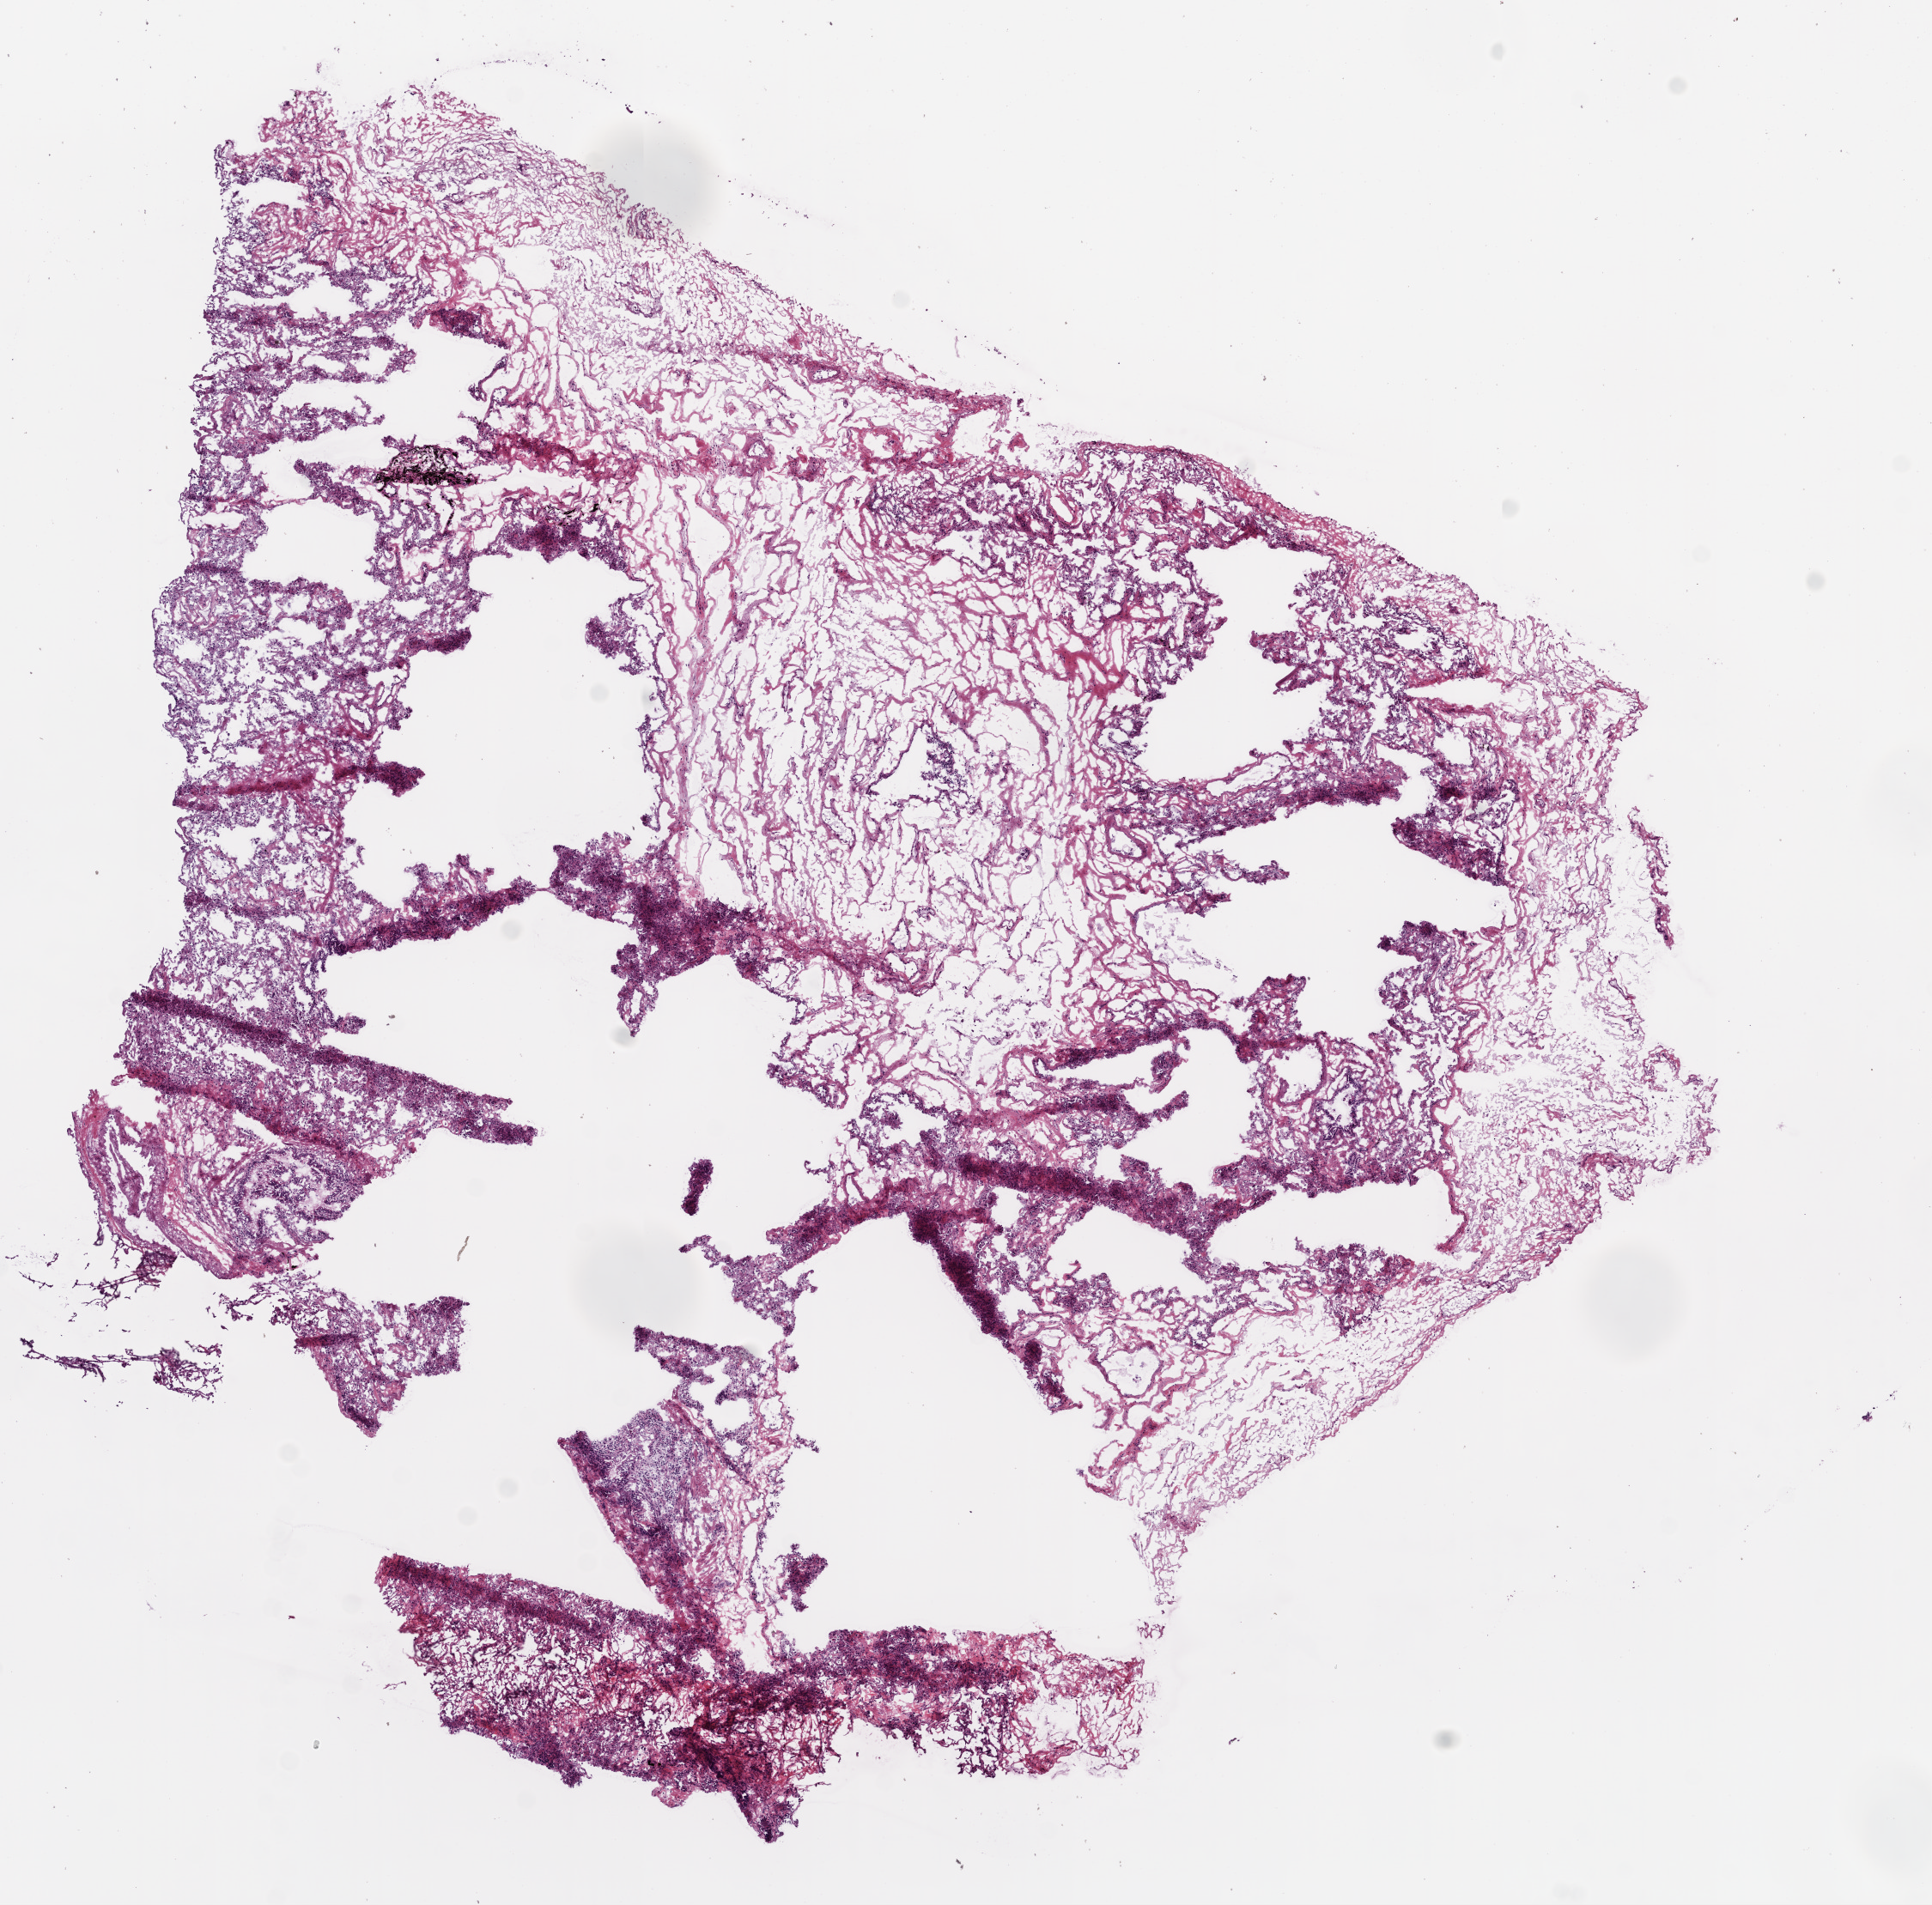
Digitized Hematoxylin and eosin (H&E) stained tissue section (whole slide) — shown as a low-resolution overview of the whole scanned area (about 9.0 x 8.9 mm, from a 20x scan). Frozen section from the bottom of the tissue portion. Sample: solid tissue normal (non-tumour tissue), lung. Patient: male, age at initial diagnosis 55 years.
* this section: solid tissue normal sample (biorepository sample class)
* patient diagnosis: Squamous cell carcinoma, NOS (lower lobe, lung)